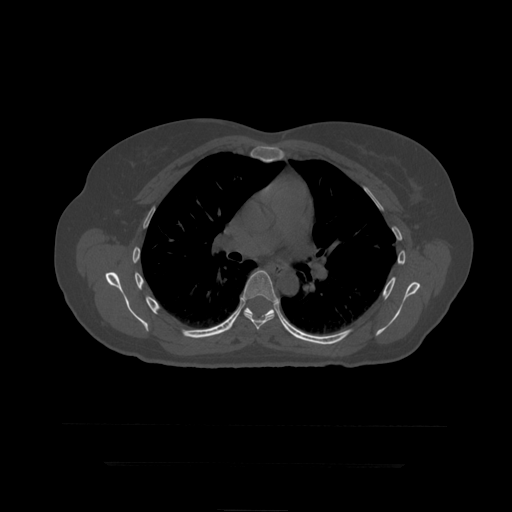
CT including the spine, one axial slice; position 296 of 399 along the scan axis; 120 kVp; bone window (W 1800 / L 400 HU); 1.25 mm slice thickness; 512 × 512 image matrix, field of view 450 × 450 mm. Patient age 41 years. Case-level facts recorded for this patient, not image findings: primary cancer: breast.
Outlined on this slice (semi-automatic segmentation, software-assisted and operator-edited):
- T7 vertebra: bounding box <242,271,278,330> (left, top, right, bottom; pixels)
- T8 vertebra: <244,308,275,316>